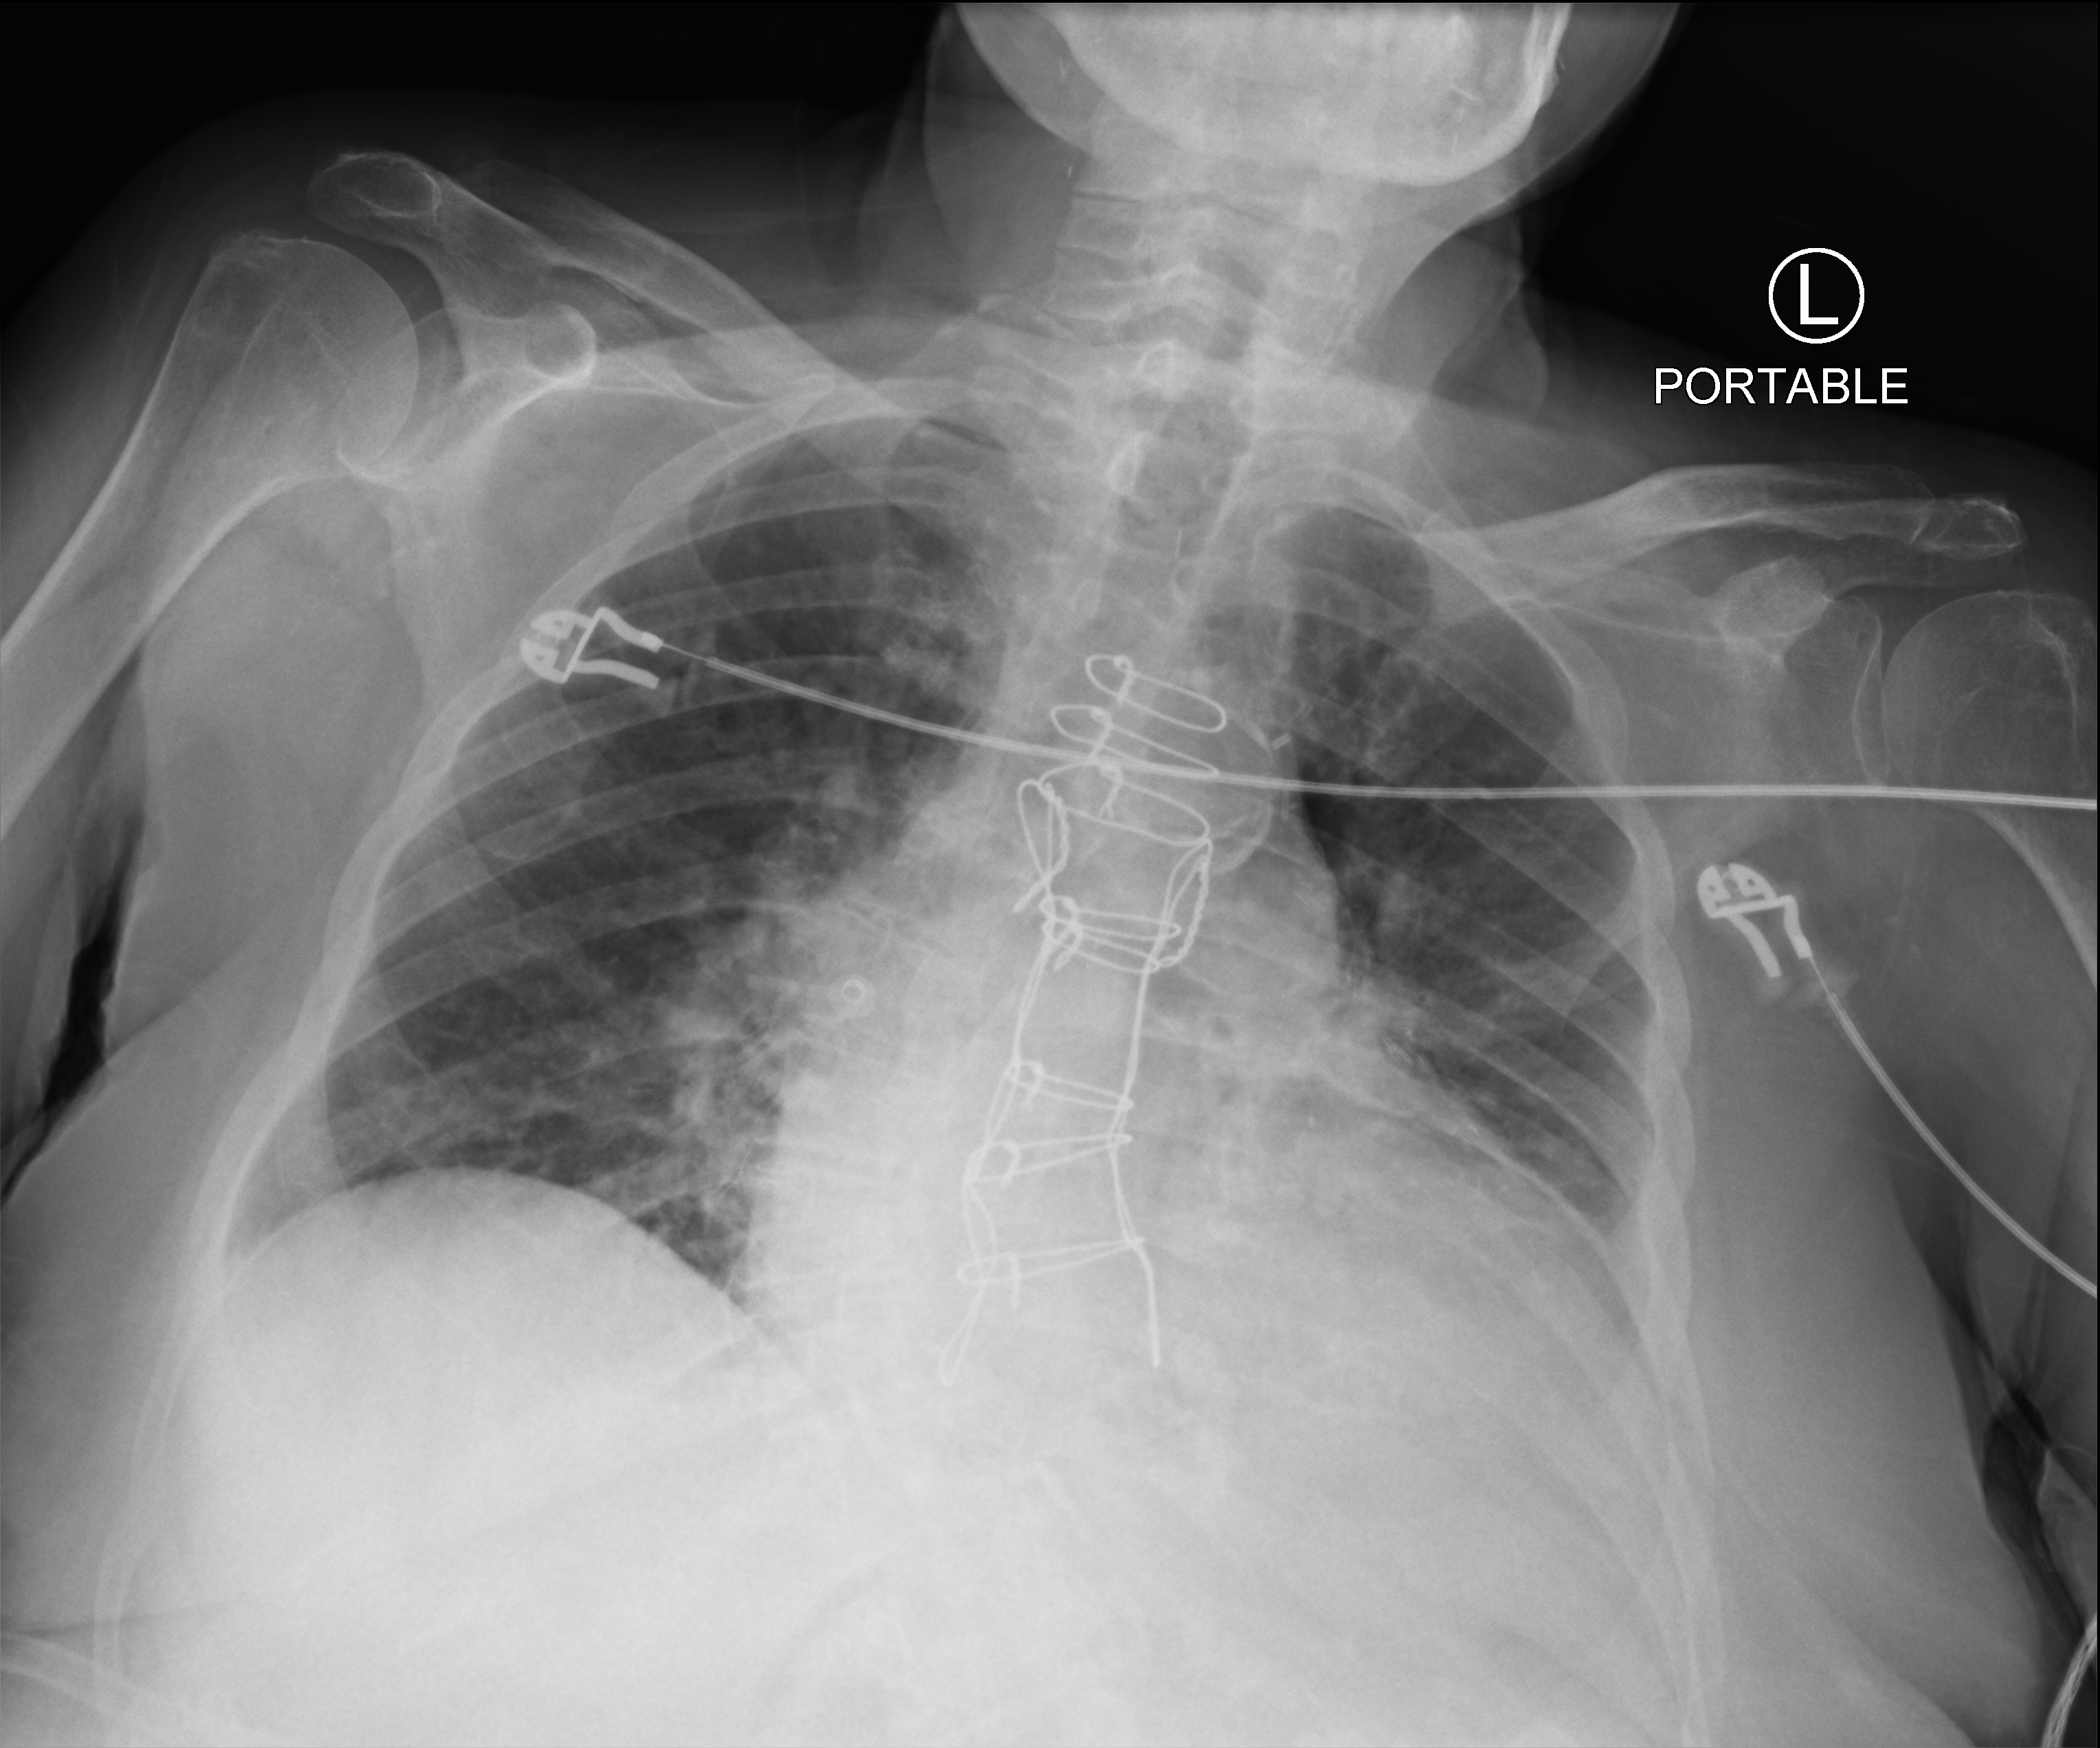
Bedside chest radiograph (computed radiography); anteroposterior (AP) projection. Patient hospitalised with COVID-19; female, aged 75–90 years.
From the hospital-stay record, not from the radiograph (when in the stay this image was taken is not recorded): length of hospital stay: 10 days; admitted to intensive care during this hospital stay: no.